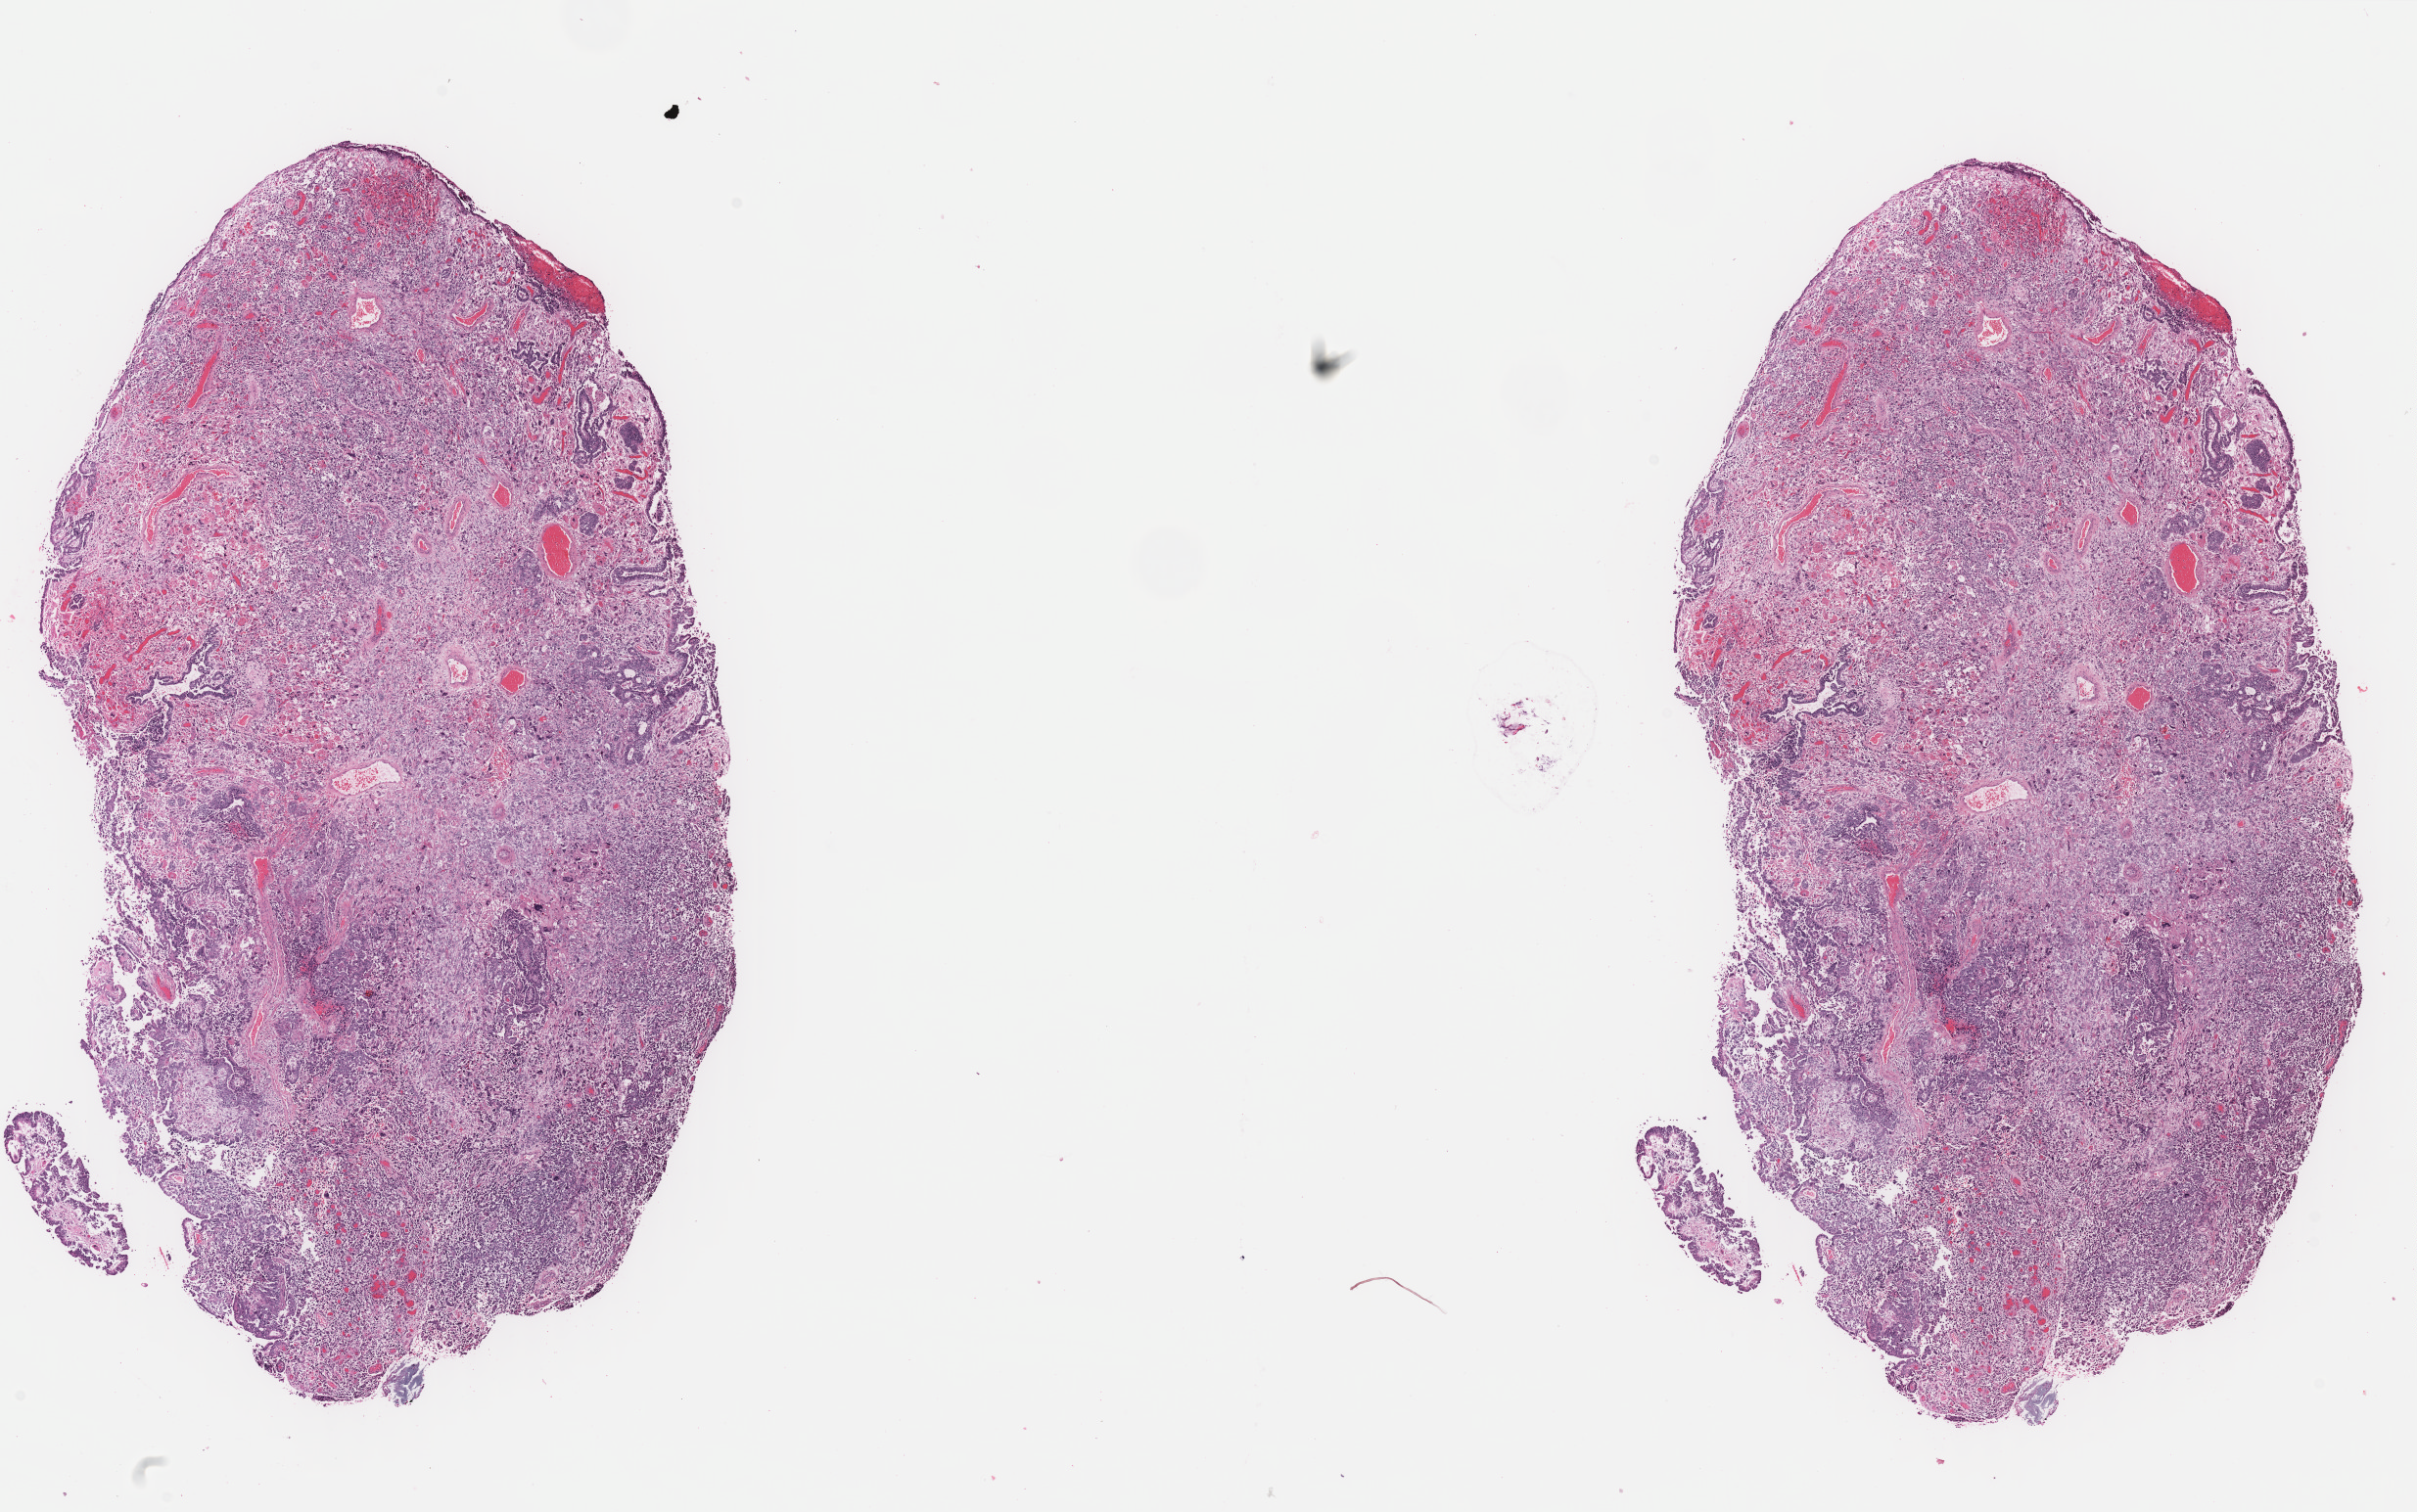
H&E whole-slide image, shown as a low-resolution overview of the whole scanned area (about 19.5 x 12.2 mm, acquisition: 40x scan). FFPE section. Uterus, primary tumour sample. Female patient; age at initial diagnosis 71 years.
FIGO stage: IA. Histologic diagnosis: Carcinosarcoma, NOS (endometrium).